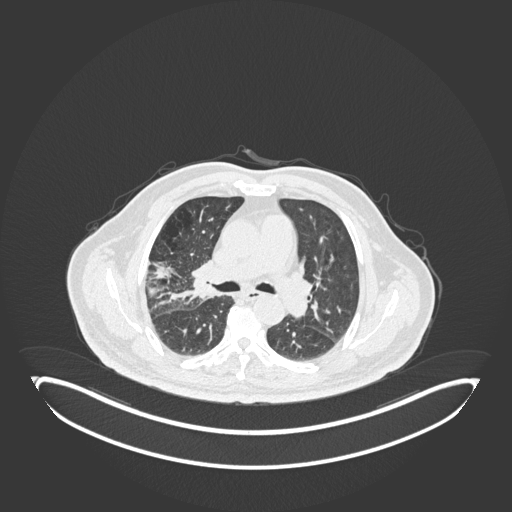
Chest CT, one axial slice; slice 105 of 247 in the series (ordered by position); reconstruction kernel B30f; lung window (W 1500 / L -600 HU); 1 mm slice thickness; 512 × 512 image matrix, field of view 500 × 500 mm. Patient: male, 72 years. From the clinical record (not read from this slice): clinical TNM (as recorded): T1c N0 M0.
Annotated regions visible in this slice (bounding box drawn by a radiologist):
- lung tumour (recorded histology: squamous cell carcinoma): bounding box (x1, y1, x2, y2) in pixels: (178, 257, 216, 307)